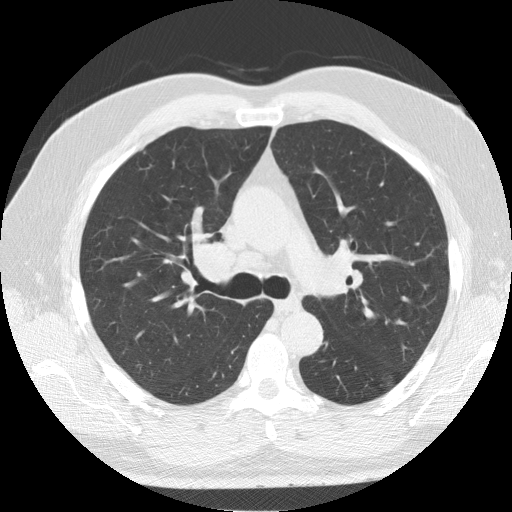
Chest CT (low-dose screening protocol), one axial image; second annual screen; lung window (W 1500 / L -600 HU); 2.5 mm slice thickness; standard (soft-tissue) reconstruction kernel (STANDARD); 512 × 512 image matrix, field of view 376 × 376 mm. Male, age 64 years at enrolment. Former smoker at enrolment.
• Lesion marked by an expert reader, bounding box (x1, y1, x2, y2) in pixels: (171, 226, 254, 304).
• The exam's reader record, not a measurement of the box and not confirmed to be the same lesion: non-calcified nodule or mass ≥4 mm, right lower lobe, 7 × 5 mm, smooth margins, soft tissue attenuation, pre-existing on the prior screen: yes; interval growth: no.